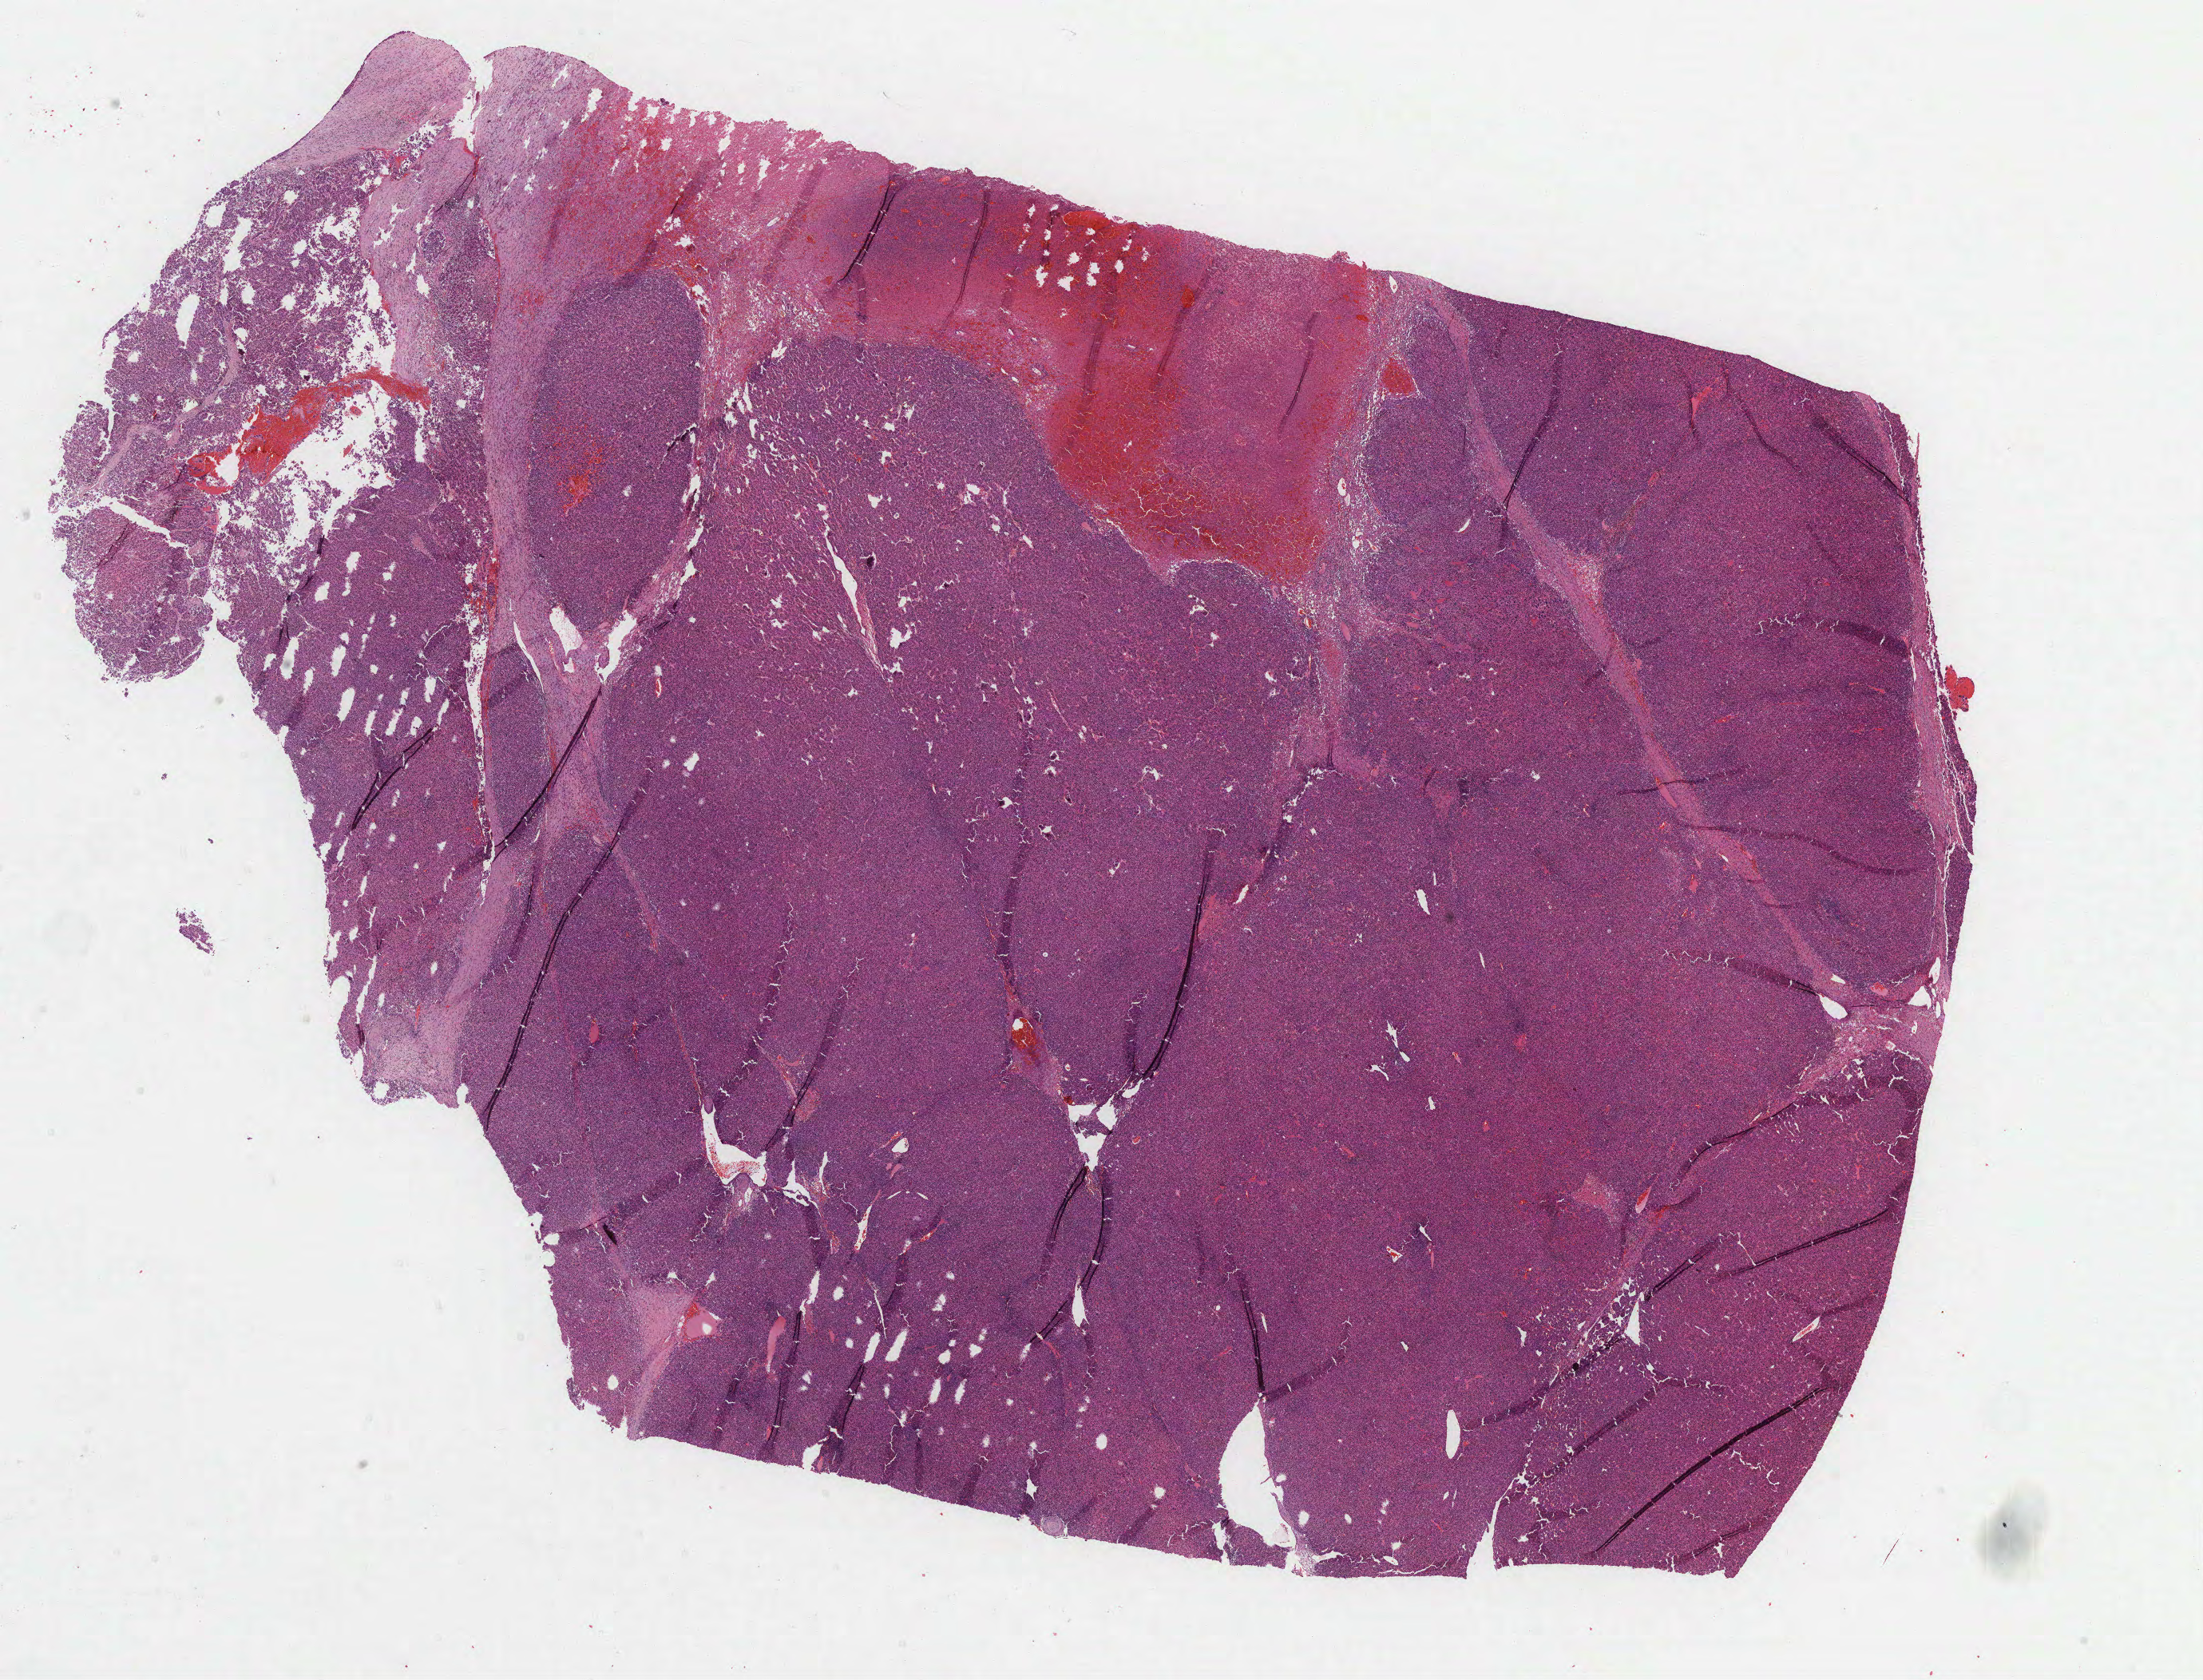
Whole-slide histology image, H&E-stained, low-resolution overview of the scanned area, about 22.3 x 17.0 mm (slide scanned at 40x), formalin-fixed paraffin-embedded (FFPE) diagnostic section, liver, primary tumour sample. Female patient; age at initial diagnosis 85 years. Histologic grade: G2 (moderately differentiated).
Diagnosis: Hepatocellular carcinoma, NOS.